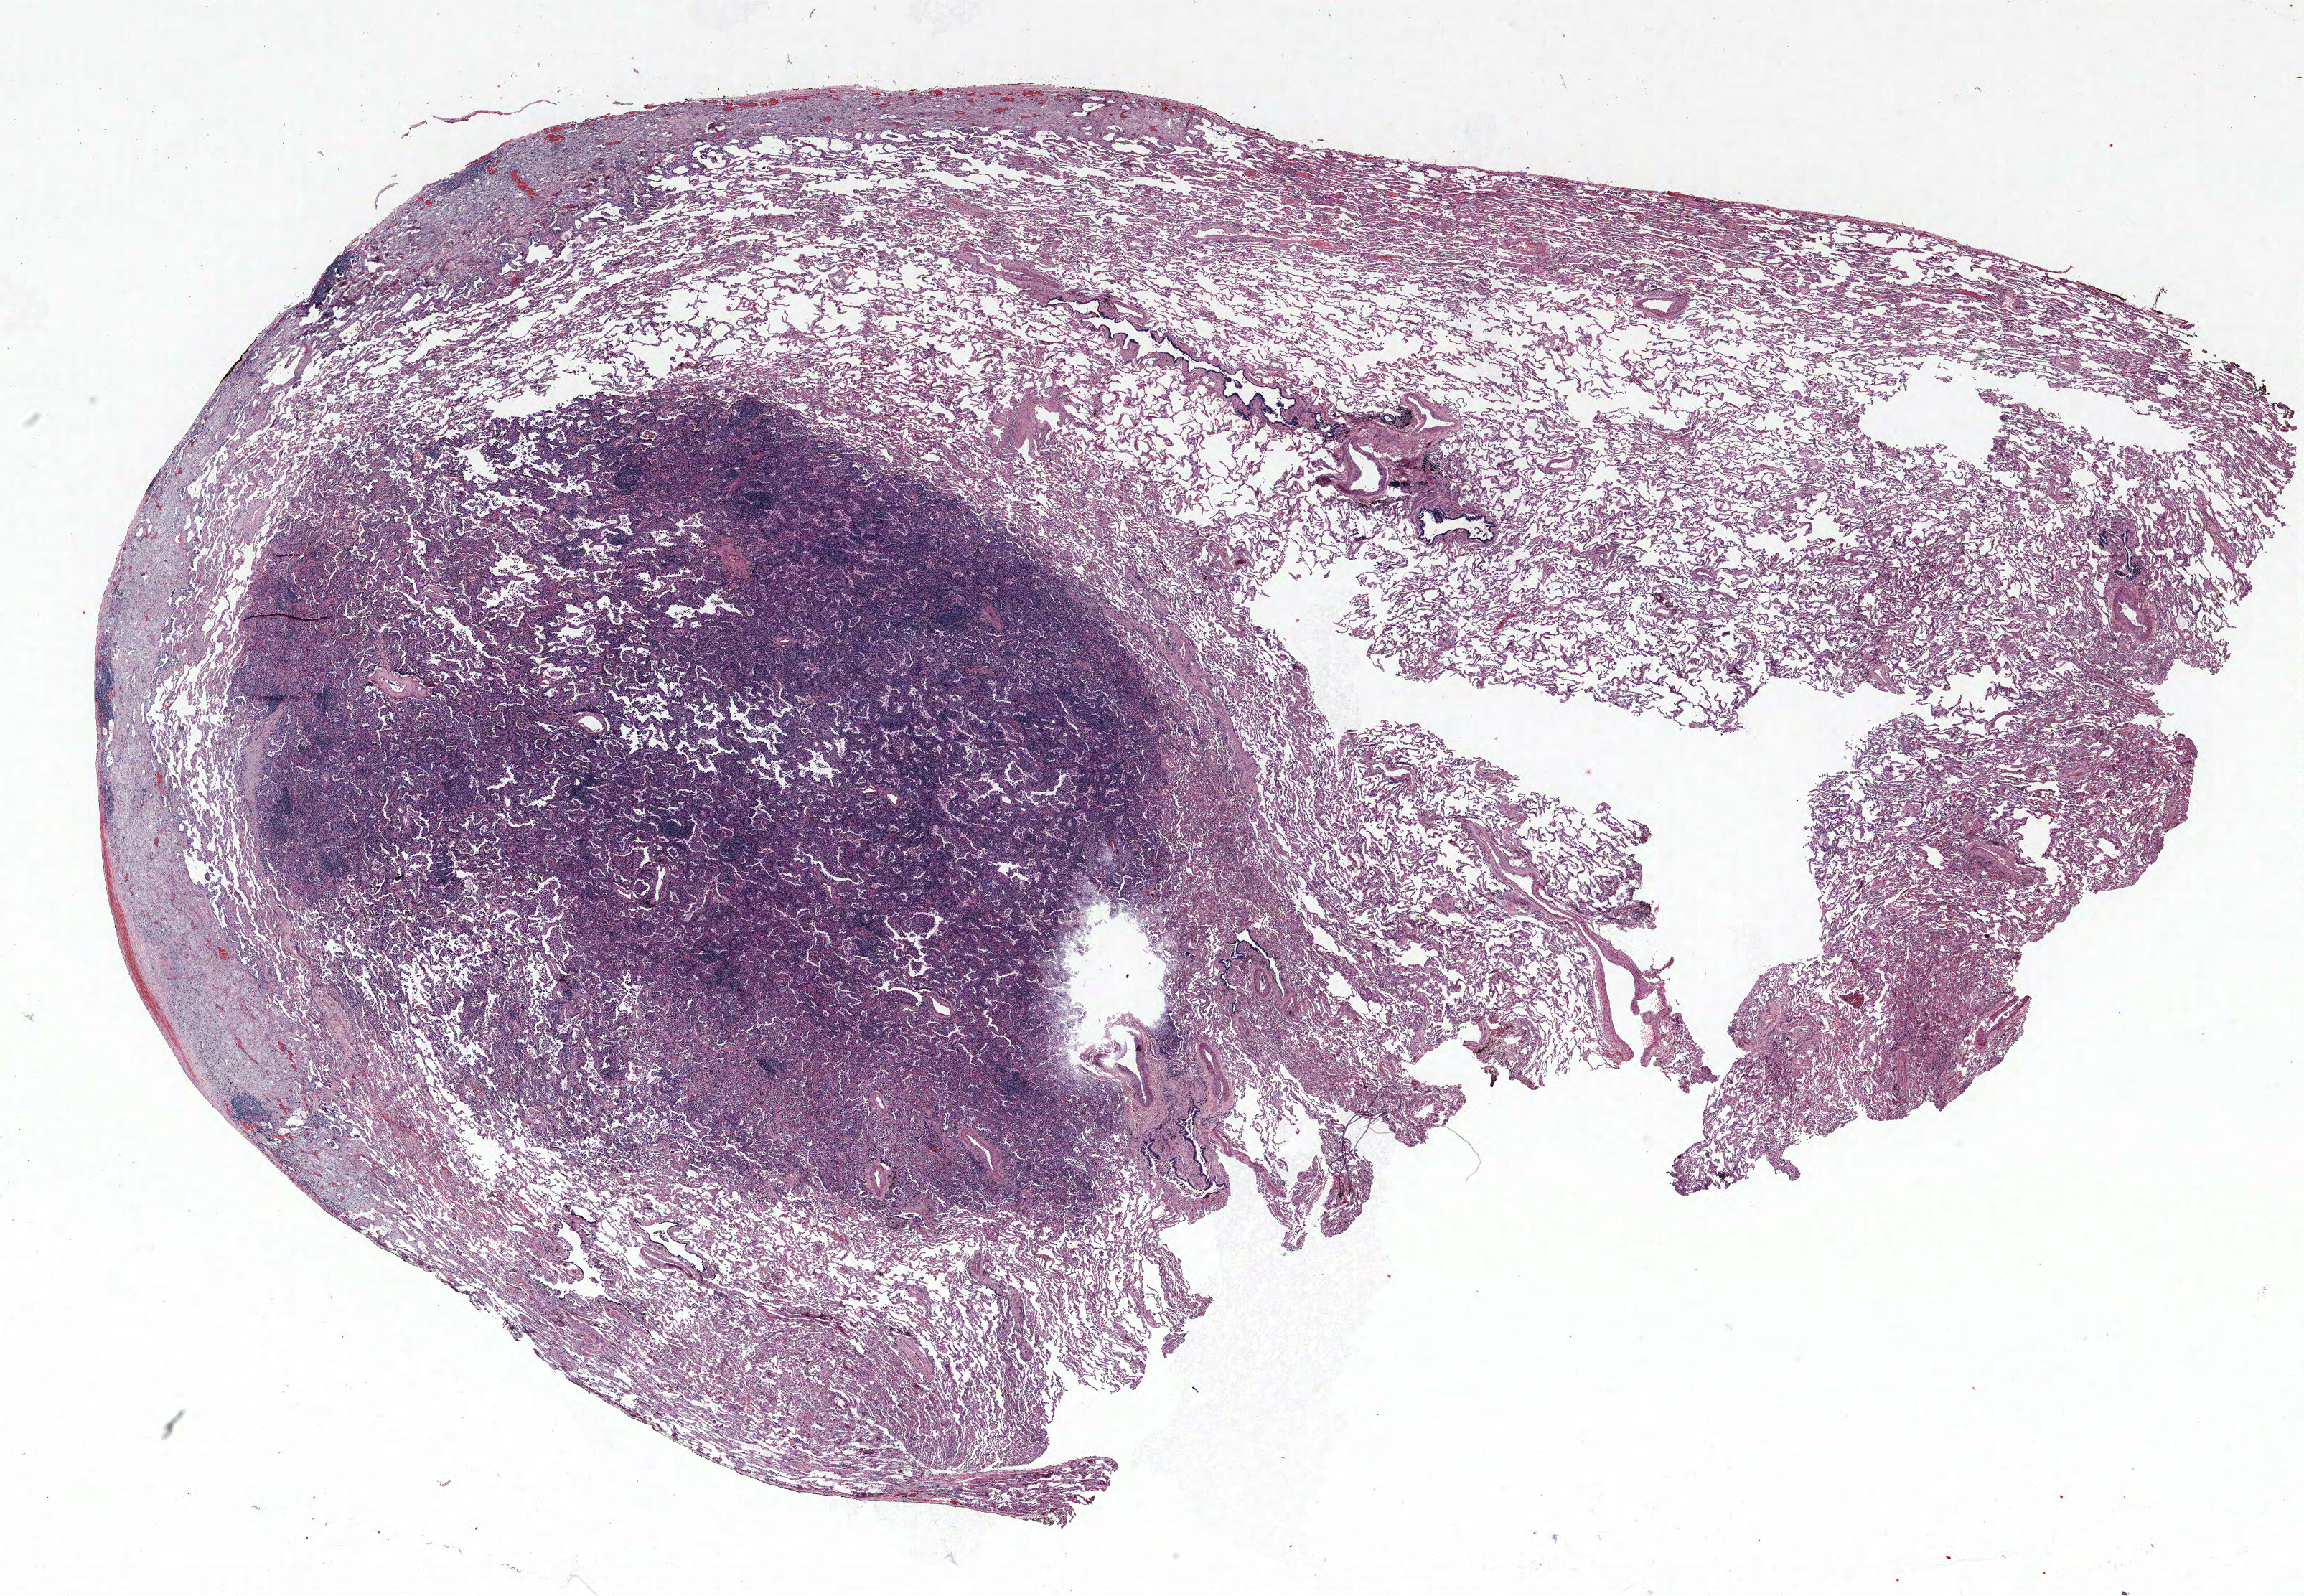
Whole-slide histology image, H&E-stained — whole scanned area (about 25.7 x 17.8 mm, from a 40x scan) shown as a low-resolution overview. Formalin-fixed paraffin-embedded (FFPE) section. Lung tissue. Male patient, aged 74 at enrolment. Former smoker at enrolment.
Participant's lung-cancer diagnosis: Bronchiolo-alveolar carcinoma, non-mucinous. Tumour size (pathology): 14 mm. Primary tumour location (clinical record): right upper lobe. ICD-O-3 topography: upper lobe of lung (C34.1). Stage (AJCC 6th edition): IA.